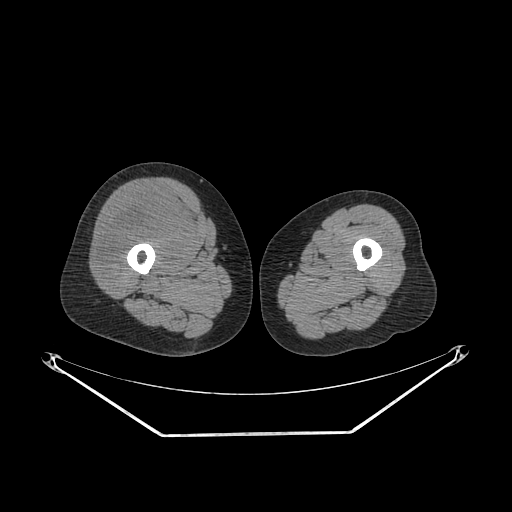
CT of an extremity soft-tissue mass (from a PET/CT study), one axial slice; position 238 of 311 along the scan axis; reconstruction kernel SOFT; soft-tissue window (W 400 / L 40 HU); 3.75 mm slice thickness; 512 × 512 image matrix, field of view 500 × 500 mm. Female patient. From the clinical record (not read from this slice): histological type: pleiomorphic undifferentiated sarcoma; grade: high; site of the primary tumour: right quadricep.
Annotated regions visible in this slice (expert contour drawn on MRI and transferred to this co-registered scan by the dataset authors):
- tumour plus oedema (research contour): bounding box [x1, y1, x2, y2] px = [100, 194, 186, 279]
- tumour (research contour): [100, 194, 186, 279]